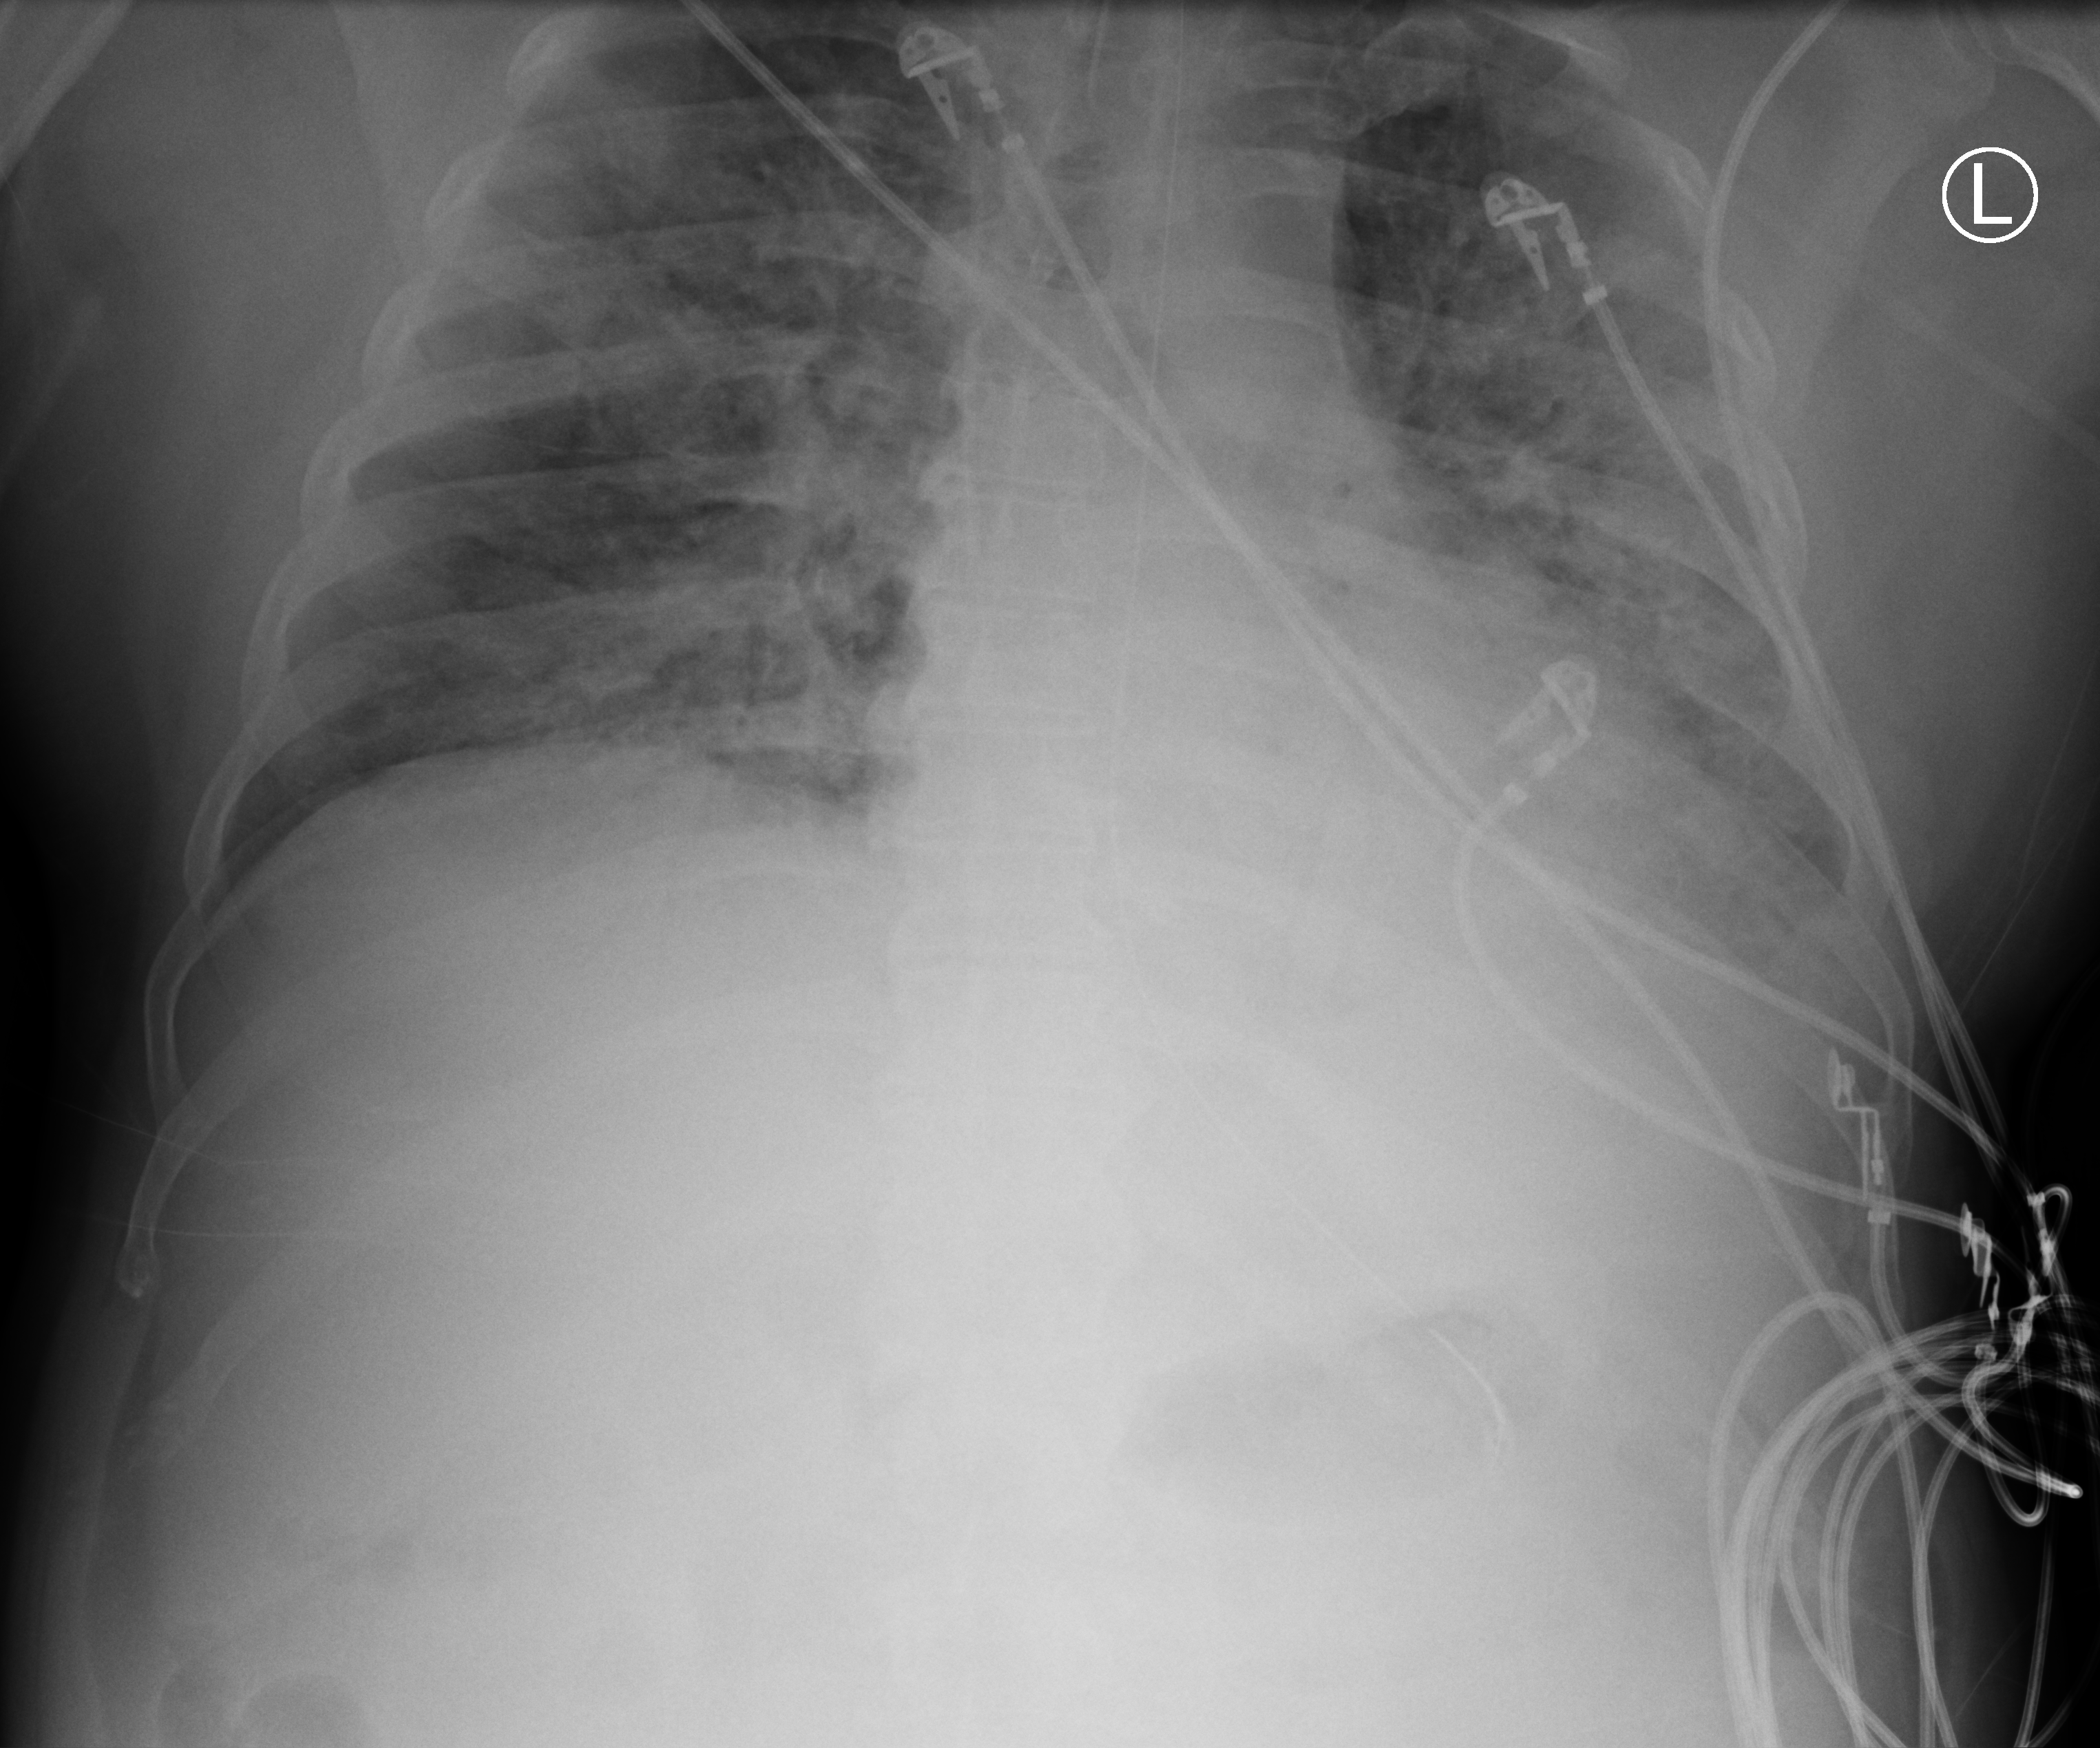
Bedside chest radiograph (computed radiography), anteroposterior (AP) projection. Patient hospitalised with COVID-19; male, aged 18–59 years.
From the hospital-stay record, not from the radiograph (when in the stay this image was taken is not recorded):
- mechanically ventilated during this hospital stay: yes